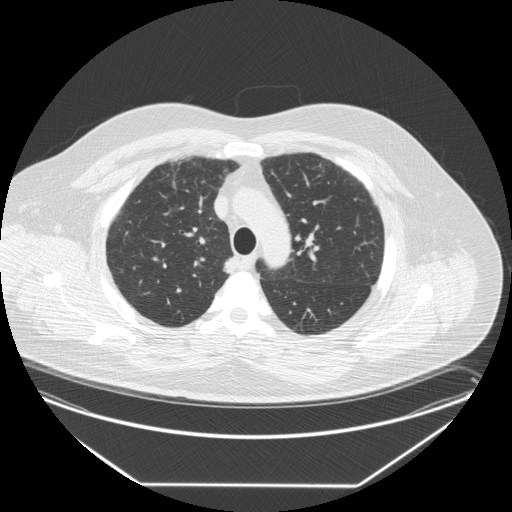
Low-dose screening chest CT, axial slice; third screening round (two years after baseline); lung window (W 1500 / L -600 HU); slice 56 of 258 in the series; 512 × 512 image matrix. Male, age 58 years at enrolment.
Lesion marked by an expert reader, box from (x=215, y=252) to (x=249, y=285) px. Reader record for this screening exam (exam-level; its link to the box is not recorded): non-calcified nodule or mass ≥4 mm, right upper lobe, 15 × 12 mm, smooth margins, soft tissue attenuation, pre-existing on the prior screen: no. Later outcome: lung cancer diagnosed 17 days after this screen — large cell carcinoma, NOS, right upper lobe, stage IV (AJCC 6th edition), 35 mm at pathology.